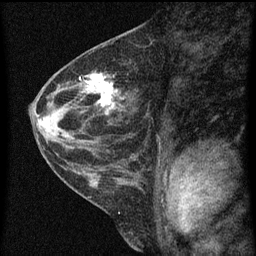
Breast MRI (dynamic contrast-enhanced), one sagittal slice; slice 28 of 60 in the series (ordered by position); dynamic contrast-enhanced series, image 2 of 3 at this slice position (ordered by acquisition); 1.5 T; TE 4.2 ms, TR 8 ms; 256 × 256 image matrix, field of view 180 × 180 mm. Patient: female, 48 years.
Annotated regions visible in this slice (semi-automatic segmentation, software-assisted and operator-edited):
- analysis volume of interest (the breast-tissue region the enhancement analysis was run in; not a lesion): bounding box <82,70,126,125> (left, top, right, bottom; pixels)
- tumour enhancement mask (voxels above the 70 % enhancement threshold inside the analysis volume of interest): <86,74,119,115>